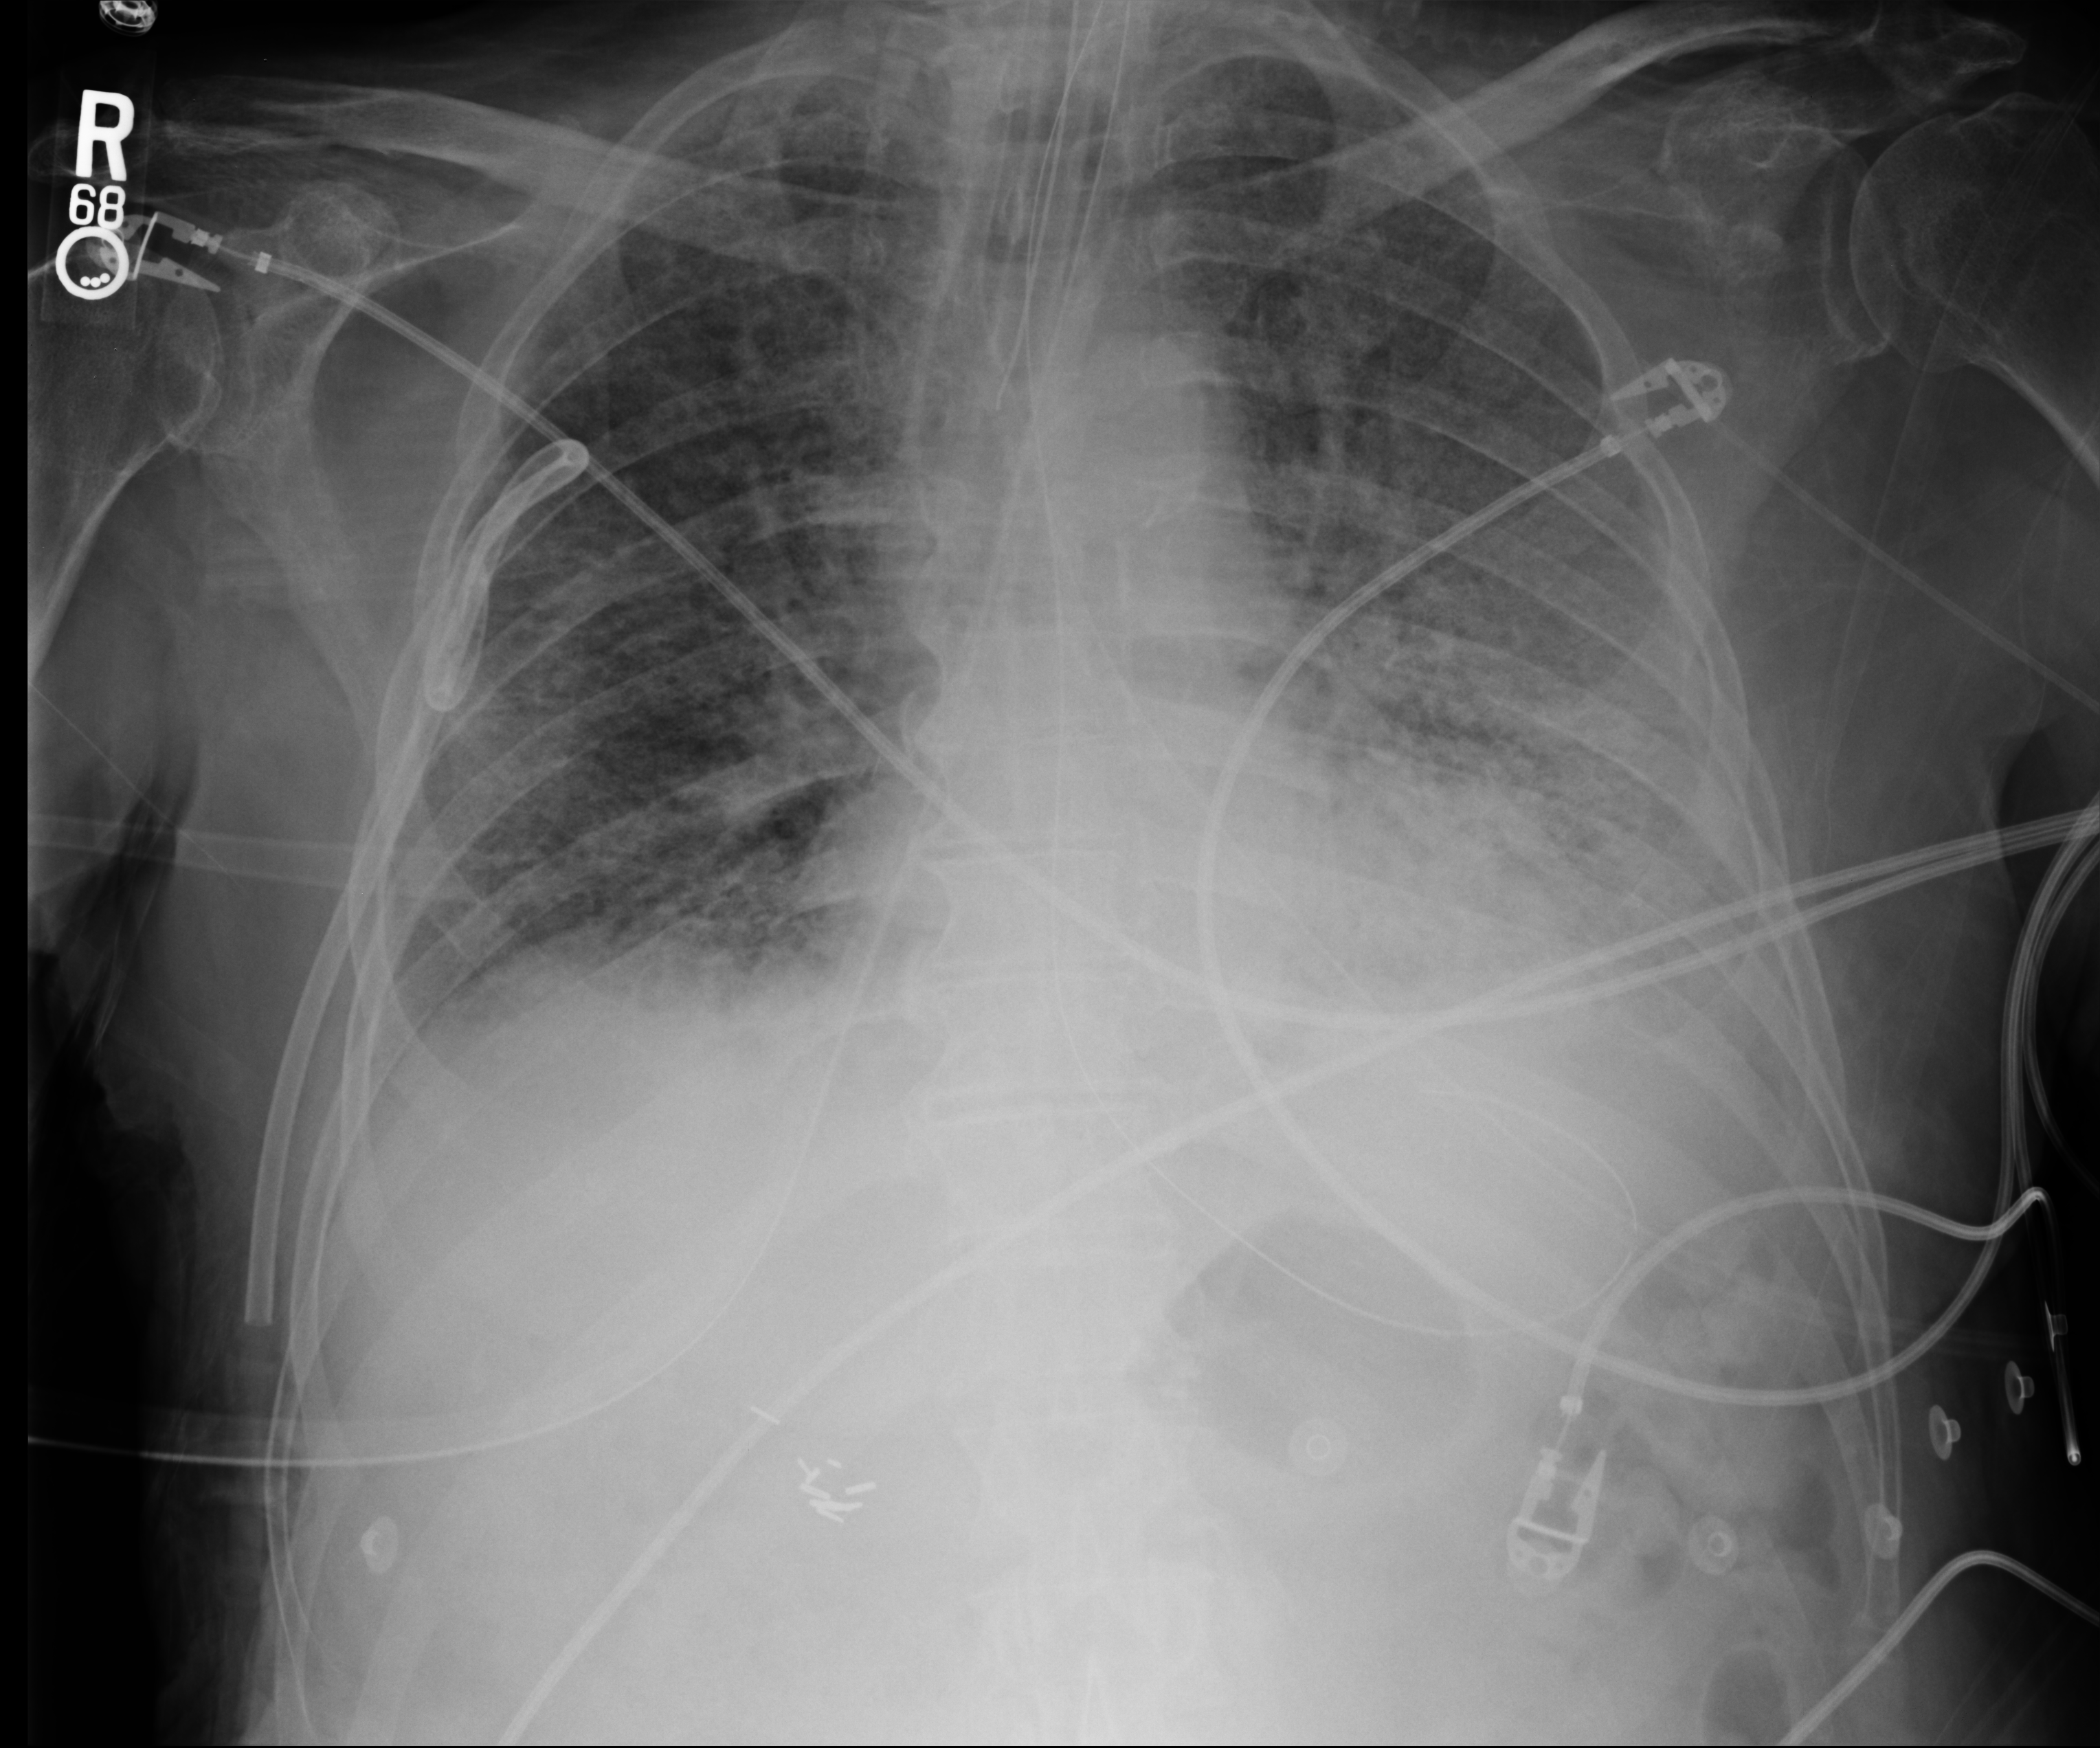
Chest X-ray (portable); anteroposterior (AP) projection. Male patient hospitalised with COVID-19, age 75–90 years.
Admission-level facts for this patient (not findings on this image; timing relative to this image not recorded):
- admitted to intensive care during this hospital stay: yes